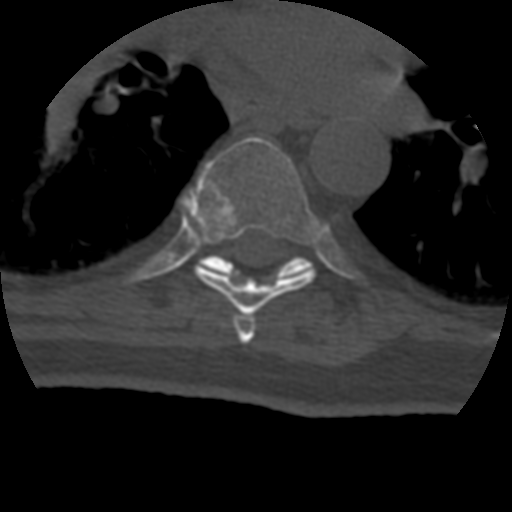
CT including the spine, one axial slice; reconstruction kernel STANDARD; bone window (W 1800 / L 400 HU); 1.25 mm slice thickness; 512 × 512 image matrix, field of view 160 × 160 mm. Patient age 69 years. From the clinical record (not read from this slice): primary cancer: prostate.
Outlined on this slice (semi-automatically segmented with operator editing):
- T6 vertebra: bounding box <233,315,256,344> (left, top, right, bottom; pixels)
- T7 vertebra: <182,136,321,318>
- T8 vertebra: <200,255,311,279>